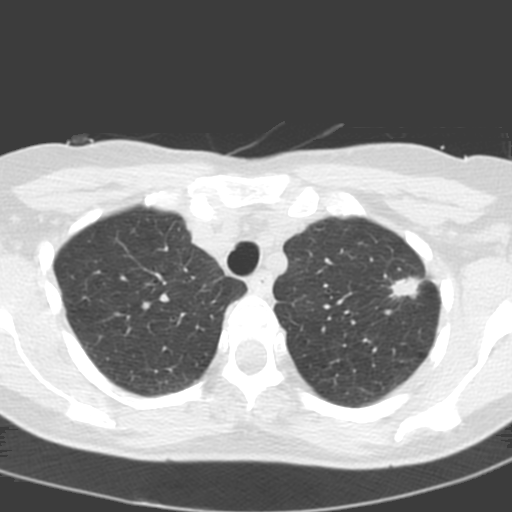
Axial slice from a low-dose chest CT screening exam. First (baseline) screen. Lung window (W 1500 / L -600 HU). 3.2 mm slice thickness. Standard (soft-tissue) reconstruction kernel (C). Slice 37 of 193 in the series. Female, age 58 years at enrolment. Current smoker at enrolment.
Lesion marked by an expert reader, bounding box [x1, y1, x2, y2] px = [379, 266, 429, 316]. Reader record for this screening exam (exam-level; its link to the box is not recorded): non-calcified nodule or mass ≥4 mm, left upper lobe, 14 × 10 mm, spiculated (stellate) margins, soft tissue attenuation. Official screen result: positive, change unspecified: nodule(s) >= 4 mm or enlarging nodule(s), mass(es), or other non-specific abnormalities suspicious for lung cancer. Participant outcome: lung cancer diagnosed 48 days after this screen — adenocarcinoma, NOS, left upper lobe, poorly differentiated (G3), stage IA (AJCC 6th edition), 13 mm at pathology.